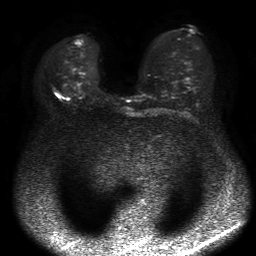
Breast MRI, one axial slice. Slice 31 of 50 in the series (ordered by position). Diffusion-weighted series; image 2 of 4 stored at this slice position (different b-values; order by instance number). 1.5 T. 4 mm slice thickness. 256 × 256 image matrix, field of view 360 × 360 mm. Female patient.
Annotated regions visible in this slice (manually delineated by an expert):
- tumour on diffusion-weighted imaging: bounding box <66,97,70,100> (left, top, right, bottom; pixels)